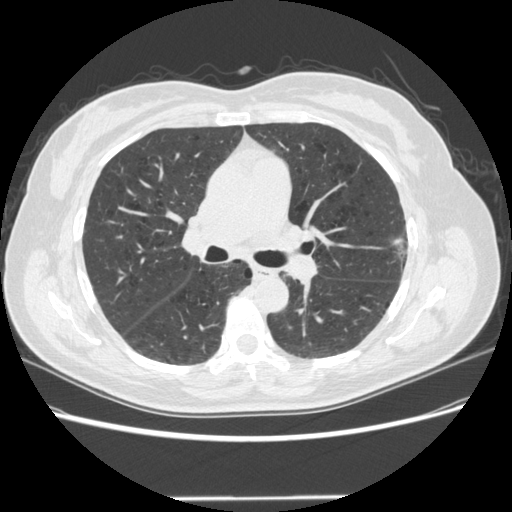
Chest CT (low-dose screening protocol), one axial image, baseline screening round, lung window (W 1500 / L -600 HU), 1.25 mm slice thickness, slice 188 of 301 in the series, 512 × 512 image matrix. Female, age 61 years at enrolment. Current smoker at enrolment.
- Expert reader's lesion annotation, bounding box <383,227,427,278> (left, top, right, bottom; pixels).
- Screening reader's record for this exam: no non-calcified nodule ≥4 mm recorded.
- Official screen result: negative screen, minor abnormalities not suspicious for lung cancer.
- Lung cancer was diagnosed 791 days after this screen: bronchiolo-alveolar adenocarcinoma, NOS, left upper lobe, well differentiated (G1), stage IA (AJCC 6th edition), 11 mm at pathology.